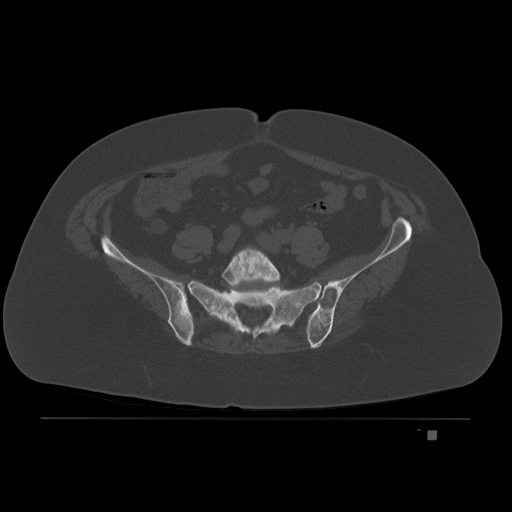
CT including the spine, one axial slice. Slice 26 of 221 in the series (ordered by position). Bone window (W 1800 / L 400 HU). 512 × 512 image matrix, field of view 474 × 474 mm. Patient: female, 63 years. Case-level facts recorded for this patient, not image findings: primary cancer: breast.
Structures marked on this image (semi-automatically segmented with operator editing):
- L5 vertebra: box from (x=221, y=246) to (x=281, y=288) px